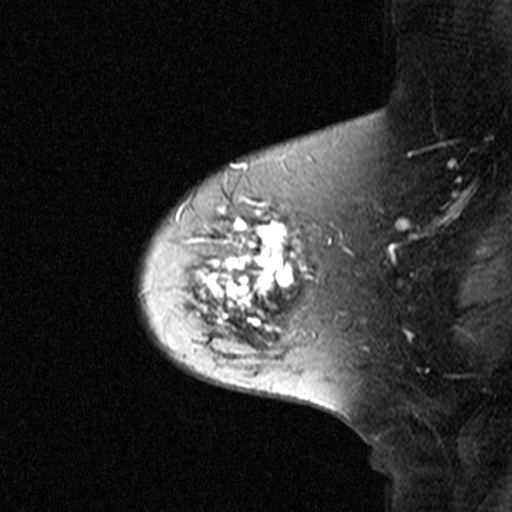
Breast MRI (dynamic contrast-enhanced), one sagittal slice; dynamic contrast-enhanced study with each time point stored as its own series, time point 2 of 3 at this slice position (early post-contrast, ordered by acquisition time); 1.5 T; TE 4.5 ms, TR 11 ms; 3 mm slice thickness; 512 × 512 image matrix. Female patient, age 65 years. From the clinical record (not read from this slice): setting: breast cancer imaged before/during neoadjuvant chemotherapy; receptor status: HER2-positive.
Structures marked on this image (semi-automatically segmented with operator editing):
- analysis volume of interest (the breast-tissue region the enhancement analysis was run in; not a lesion): bounding box <160,172,329,345> (left, top, right, bottom; pixels)
- tumour enhancement mask (voxels above the 90 % enhancement threshold inside the analysis volume of interest): <190,197,308,332>